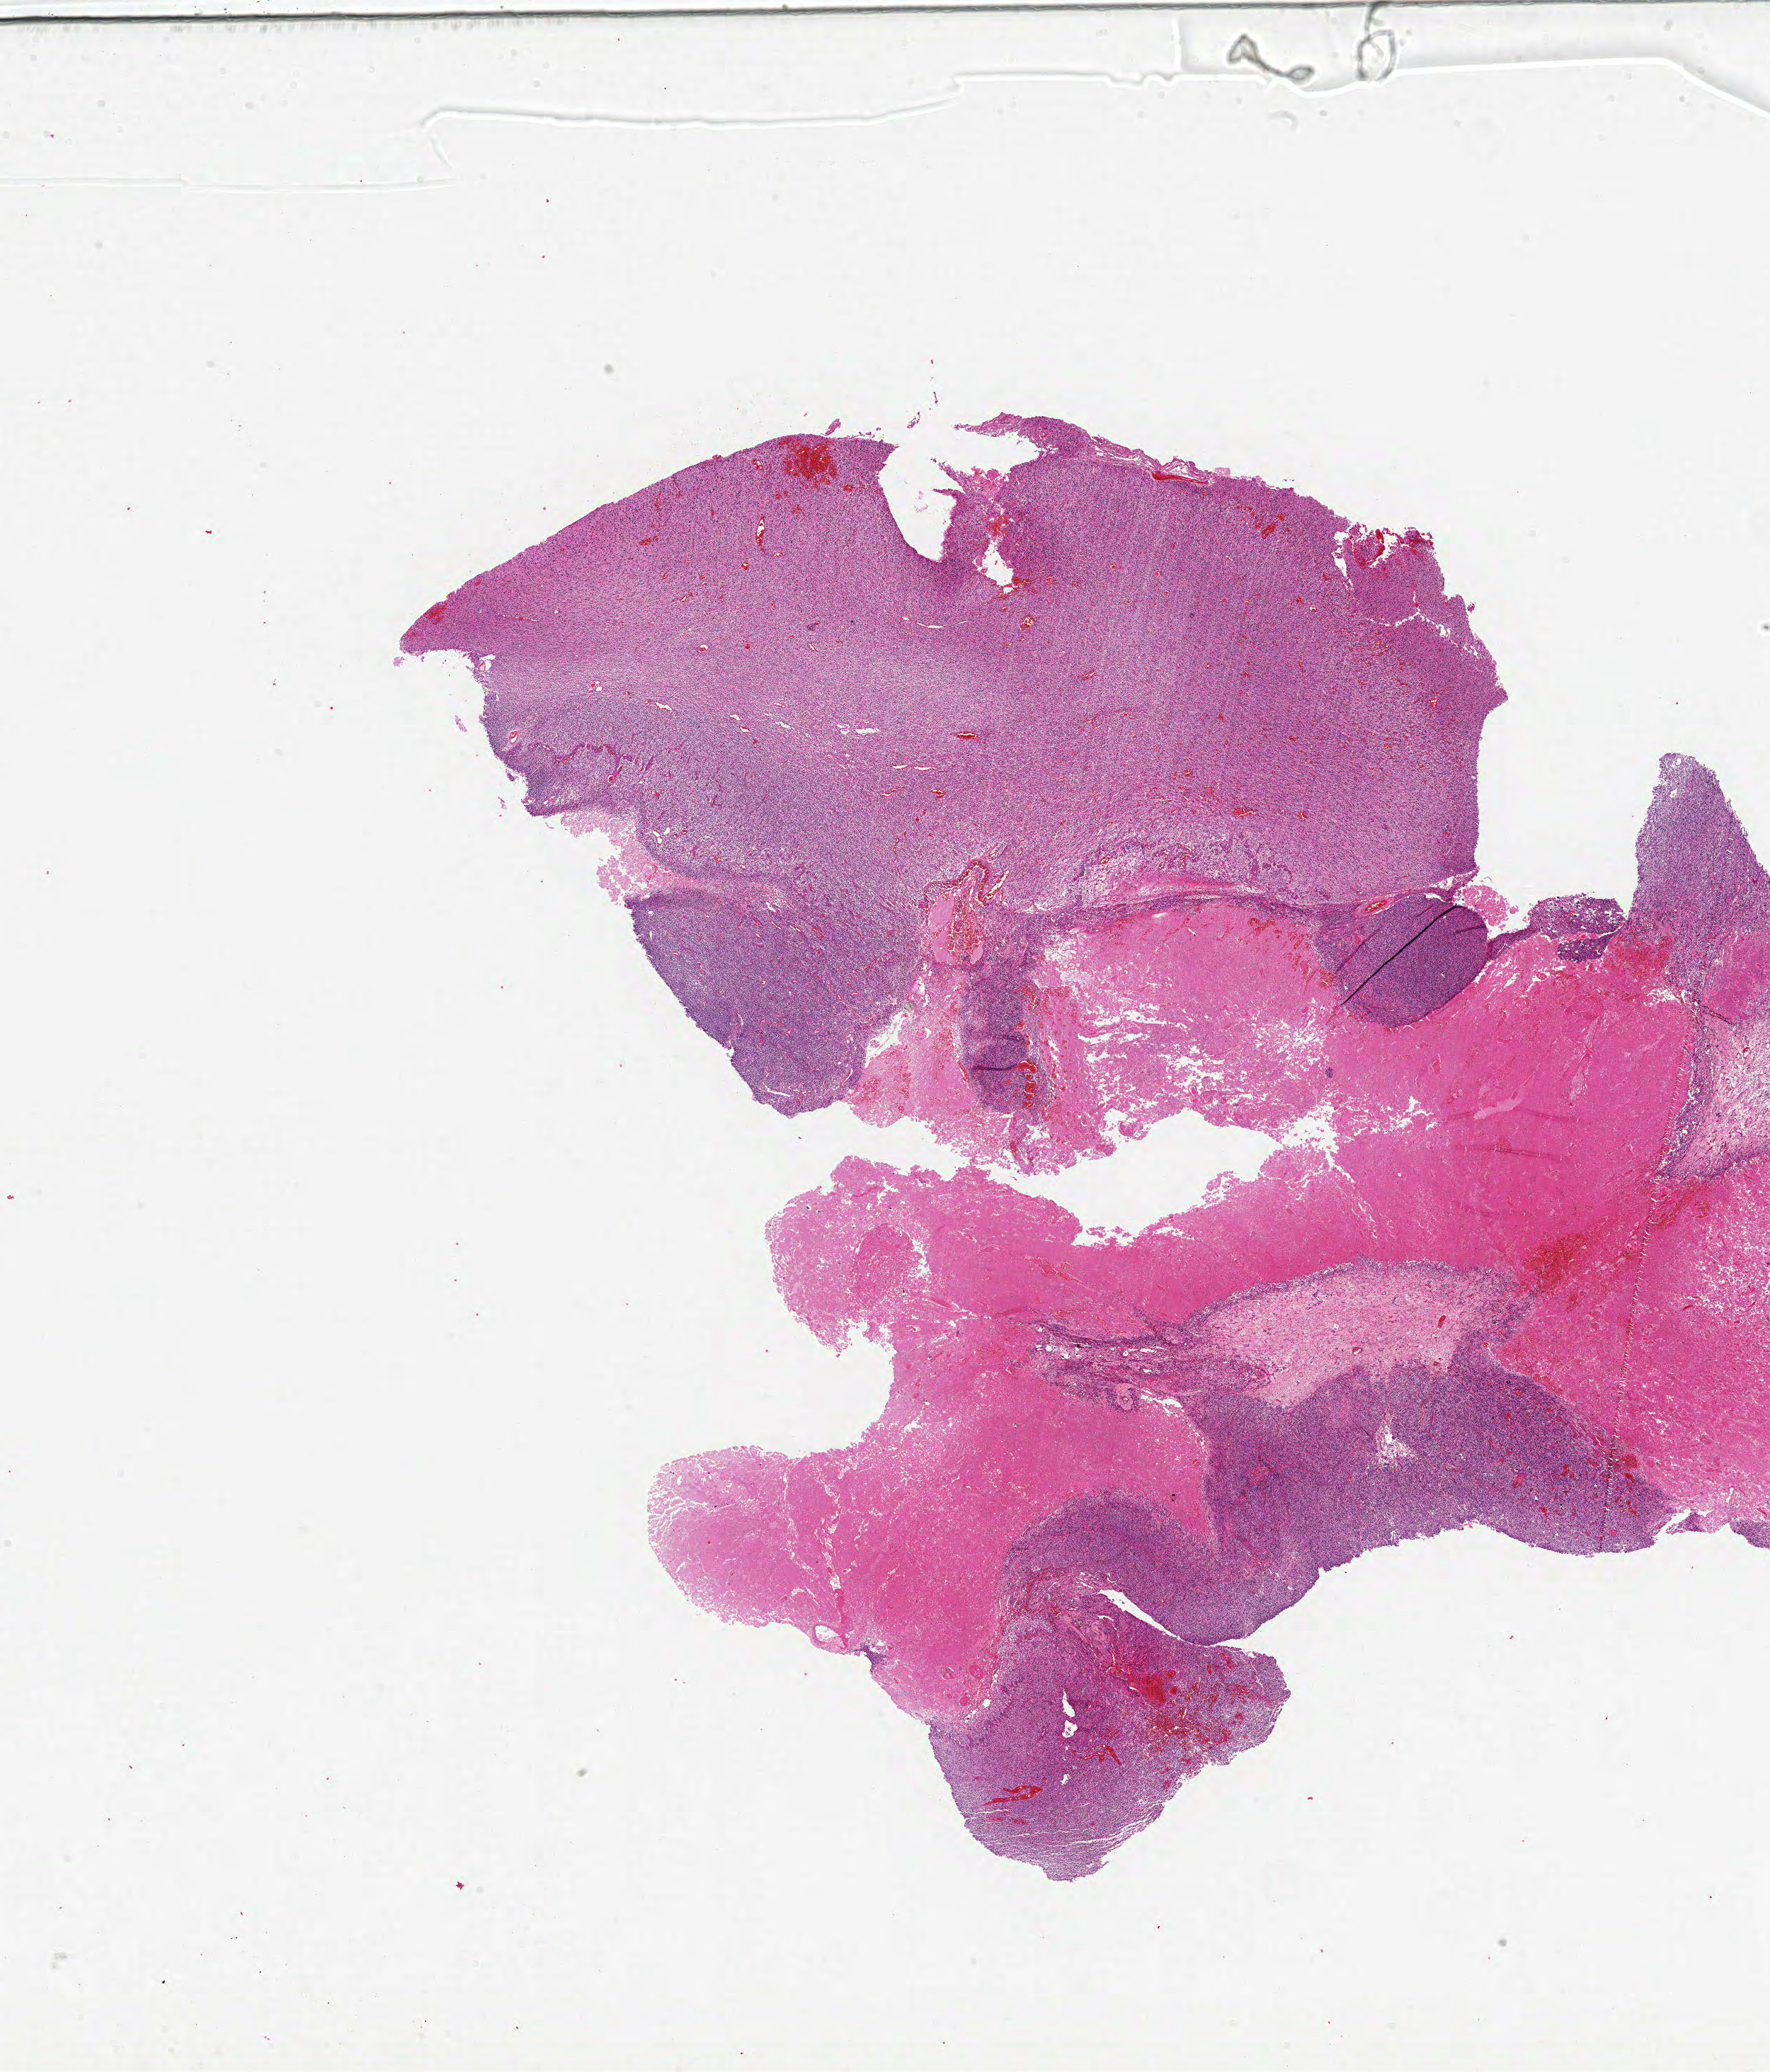
Hematoxylin and eosin (H&E) stained whole-slide image, shown as a low-resolution overview of the whole scanned area (about 20.0 x 23.4 mm, slide scanned at 20x); formalin-fixed paraffin-embedded (FFPE) diagnostic section; primary tumour sample from the brain. Male patient; age at initial diagnosis 60 years.
Histologic diagnosis: Glioblastoma.